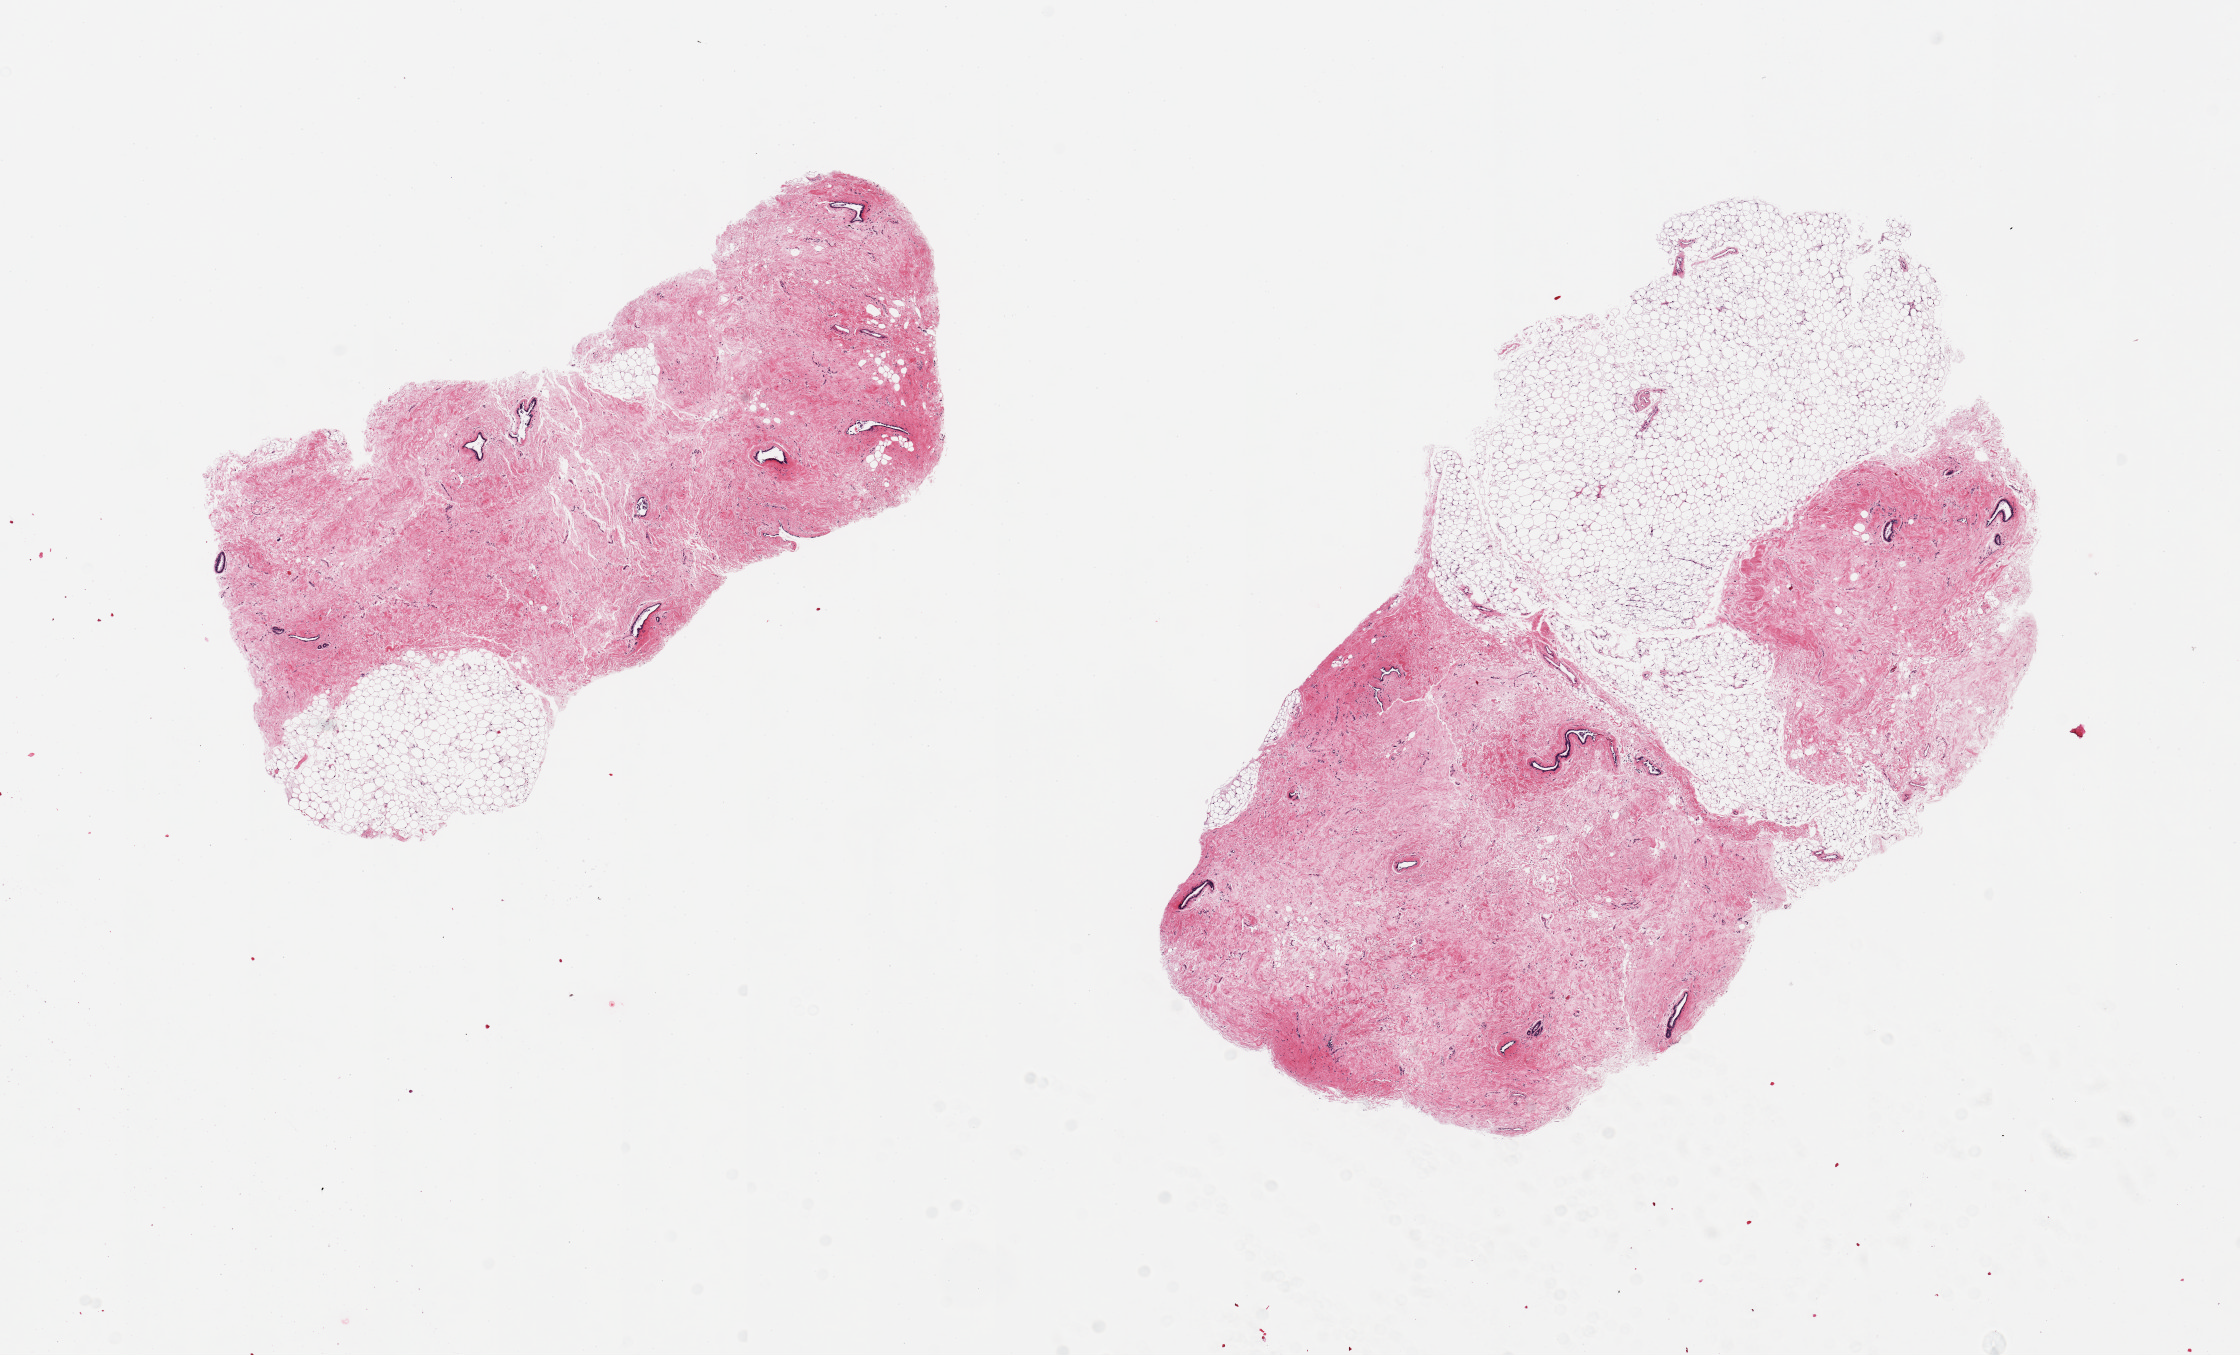
Digitized H&E-stained section — shown as a low-resolution overview of the whole scanned area (about 17.7 x 10.7 mm); PAXgene-fixed, paraffin-embedded tissue; section of breast (target tissue); donor tissue sample.
• reviewer comment on this tissue sample: 2 pieces; increased ducts in fibrous stroma consistent with gynecomastoid hyperplasia; fat comprises 15% & 40%